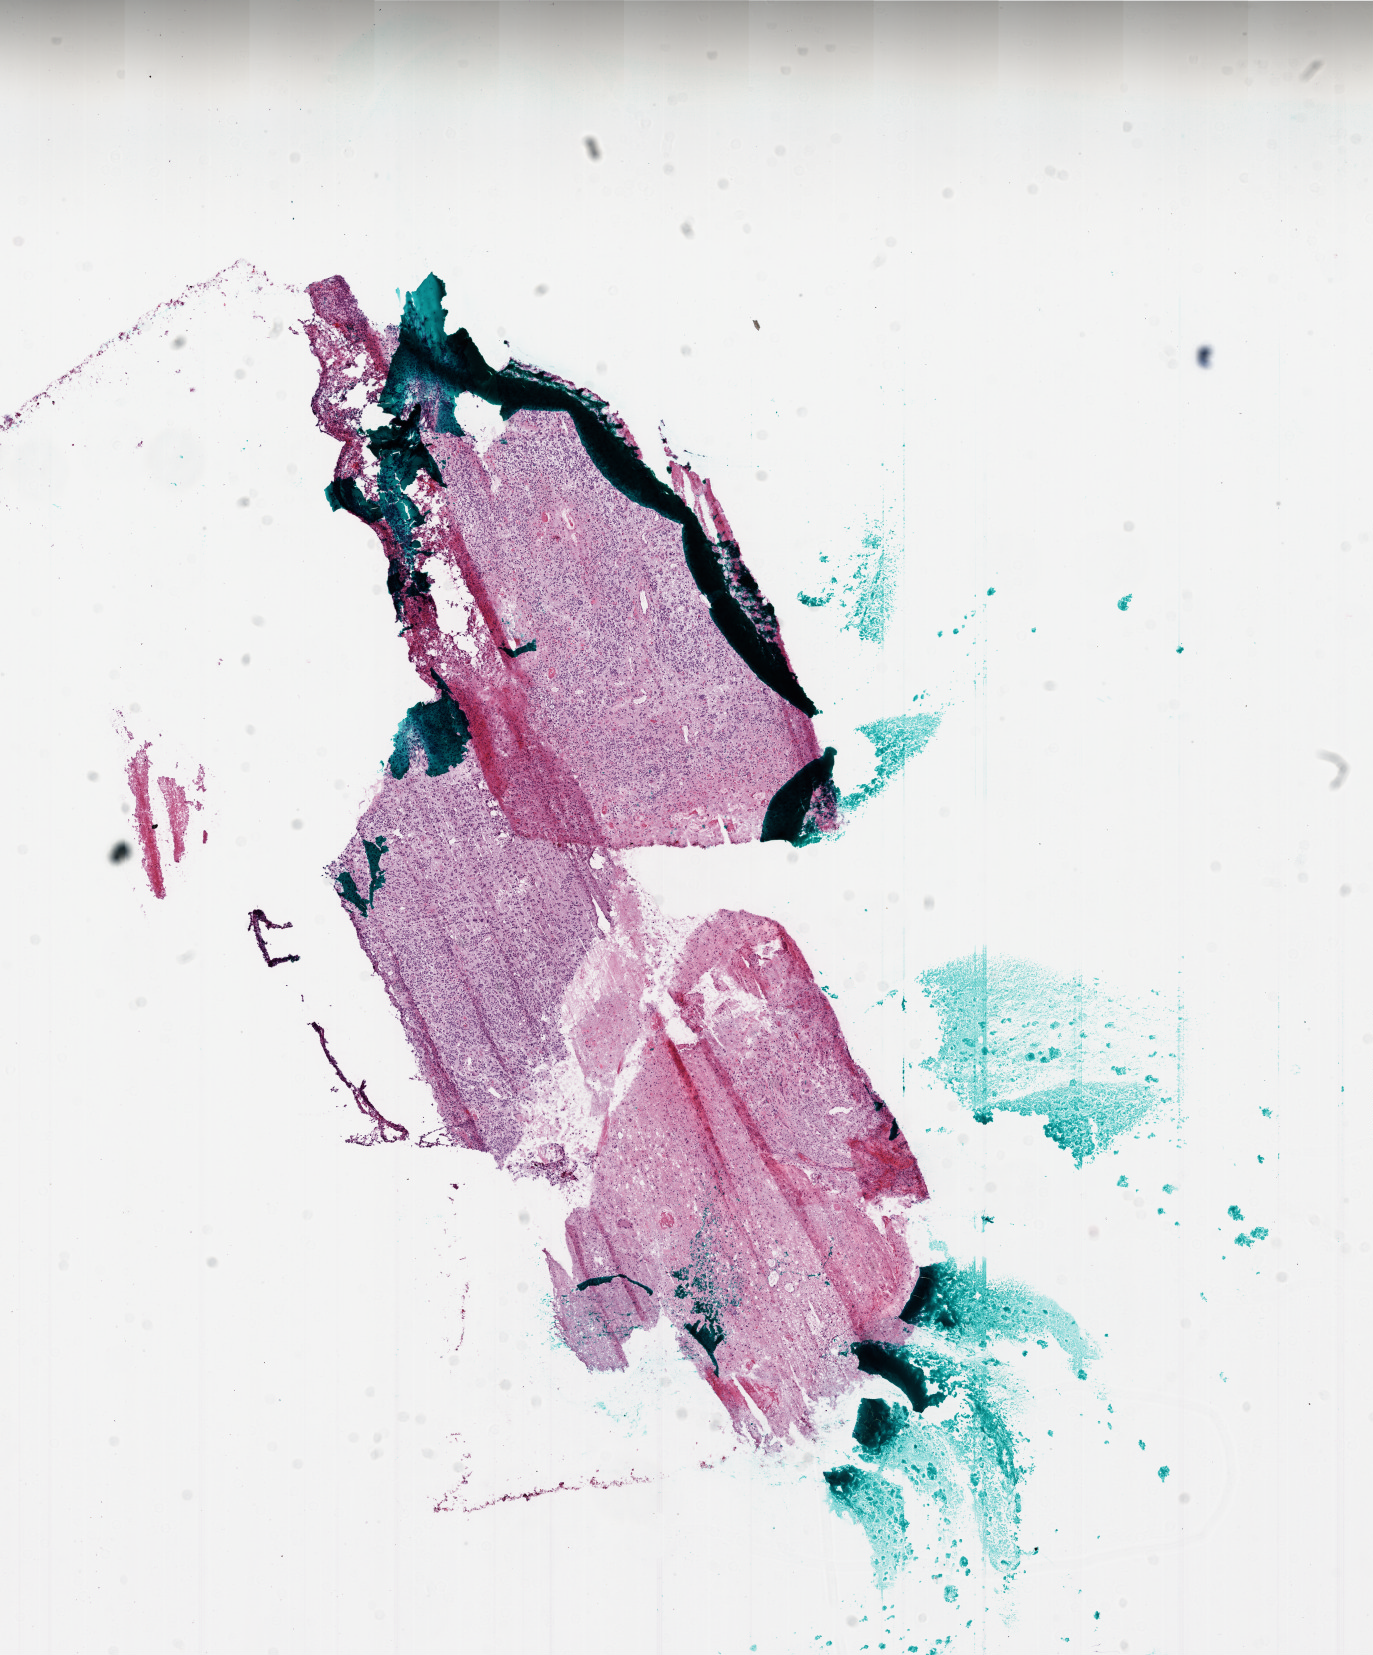
Digitized H&E tissue section (whole slide) — low-resolution overview of the scanned area, about 11.0 x 13.2 mm (acquisition: 20x scan); frozen section; brain, primary tumour sample. Female, age 72 years at initial diagnosis. Pathologist review of this section (percent, as recorded): tumour cells 50%, tumour nuclei 90%.
Pathologic diagnosis: Glioblastoma.